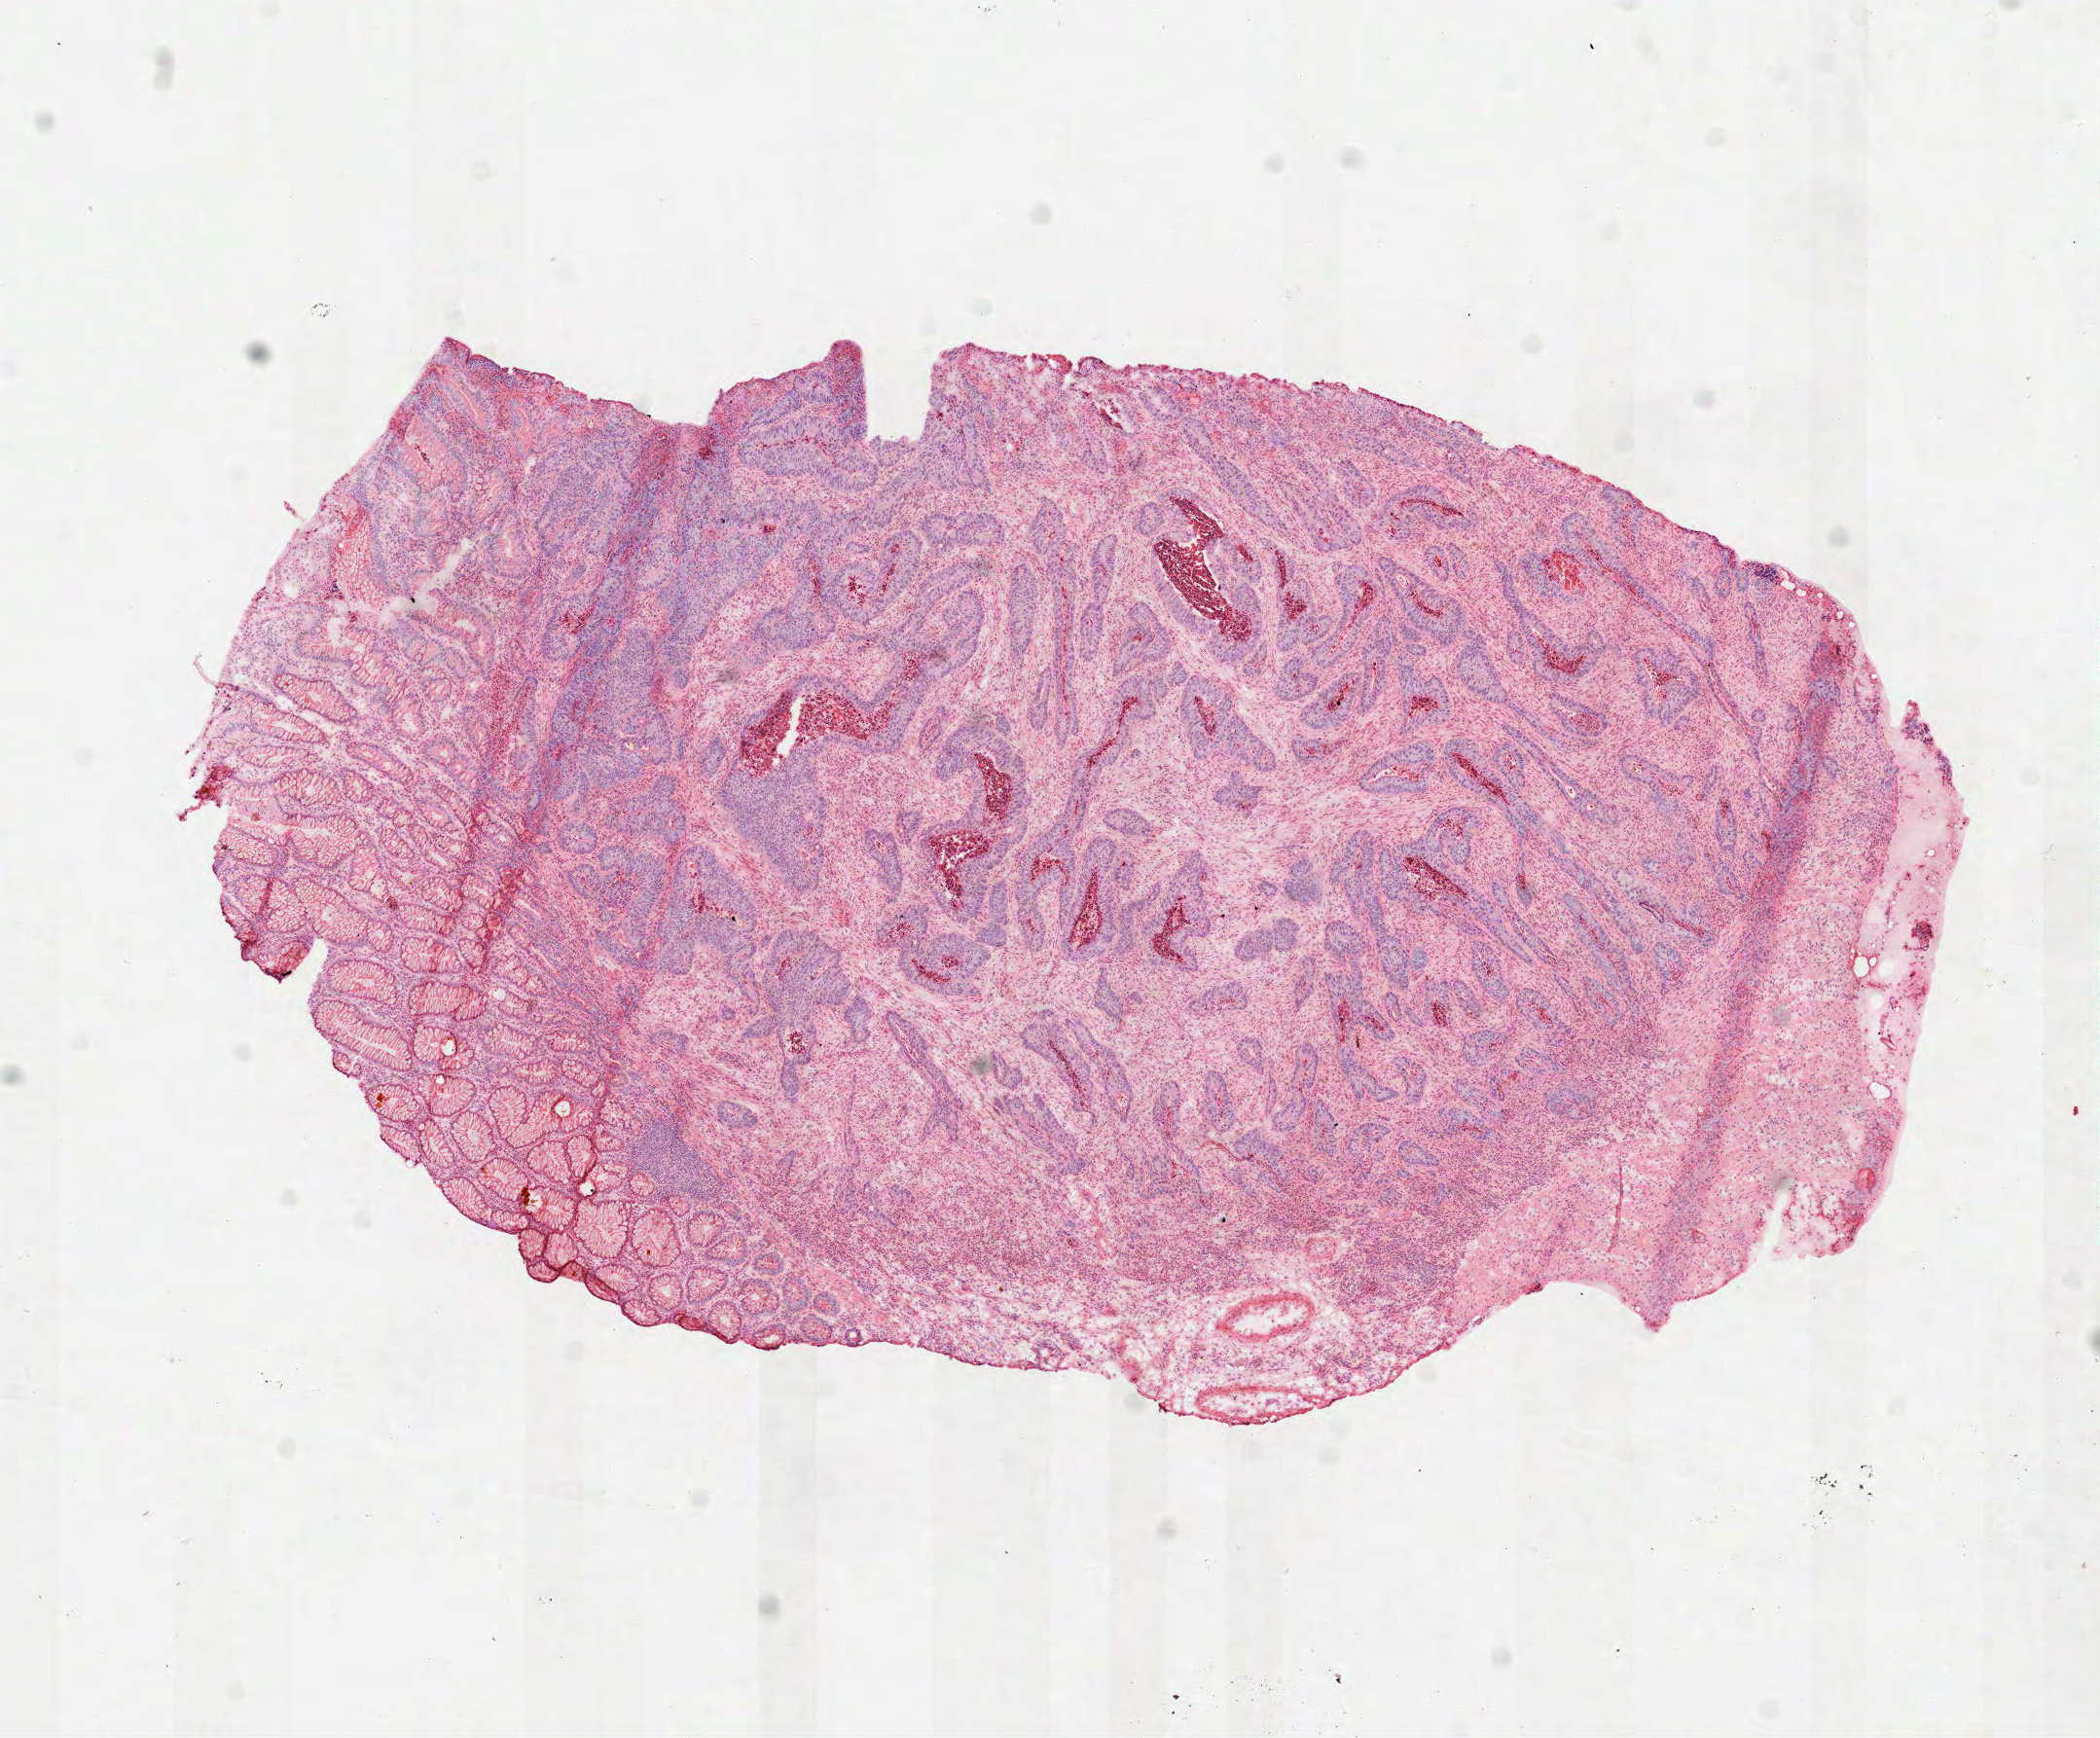
H&E-stained whole-slide image — shown as a low-resolution overview of the whole scanned area (about 8.7 x 7.2 mm, from a 40x scan). Frozen section. Sample: primary tumour, rectum. Patient: female, age at initial diagnosis 78 years. Composition of this section per pathologist review: tumour cells 62%, tumour nuclei 70%, normal cells 10%, stromal cells 20%, necrosis 8%.
AJCC pathologic stage: IIA (7th edition). Lymph nodes positive (case pathology): 0 of 19 examined. Pathologic diagnosis: Tubular adenocarcinoma.